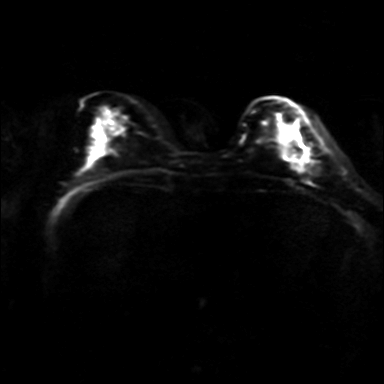
Breast MRI, one axial slice. Position 13 of 36 along the scan axis. Diffusion-weighted series; image 2 of 4 stored at this slice position (different b-values; order by instance number). 3 T. 384 × 384 image matrix. Female patient.
Structures marked on this image (outlined manually by an expert reader):
- tumour on diffusion-weighted imaging: bounding box [x1, y1, x2, y2] px = [287, 142, 299, 159]